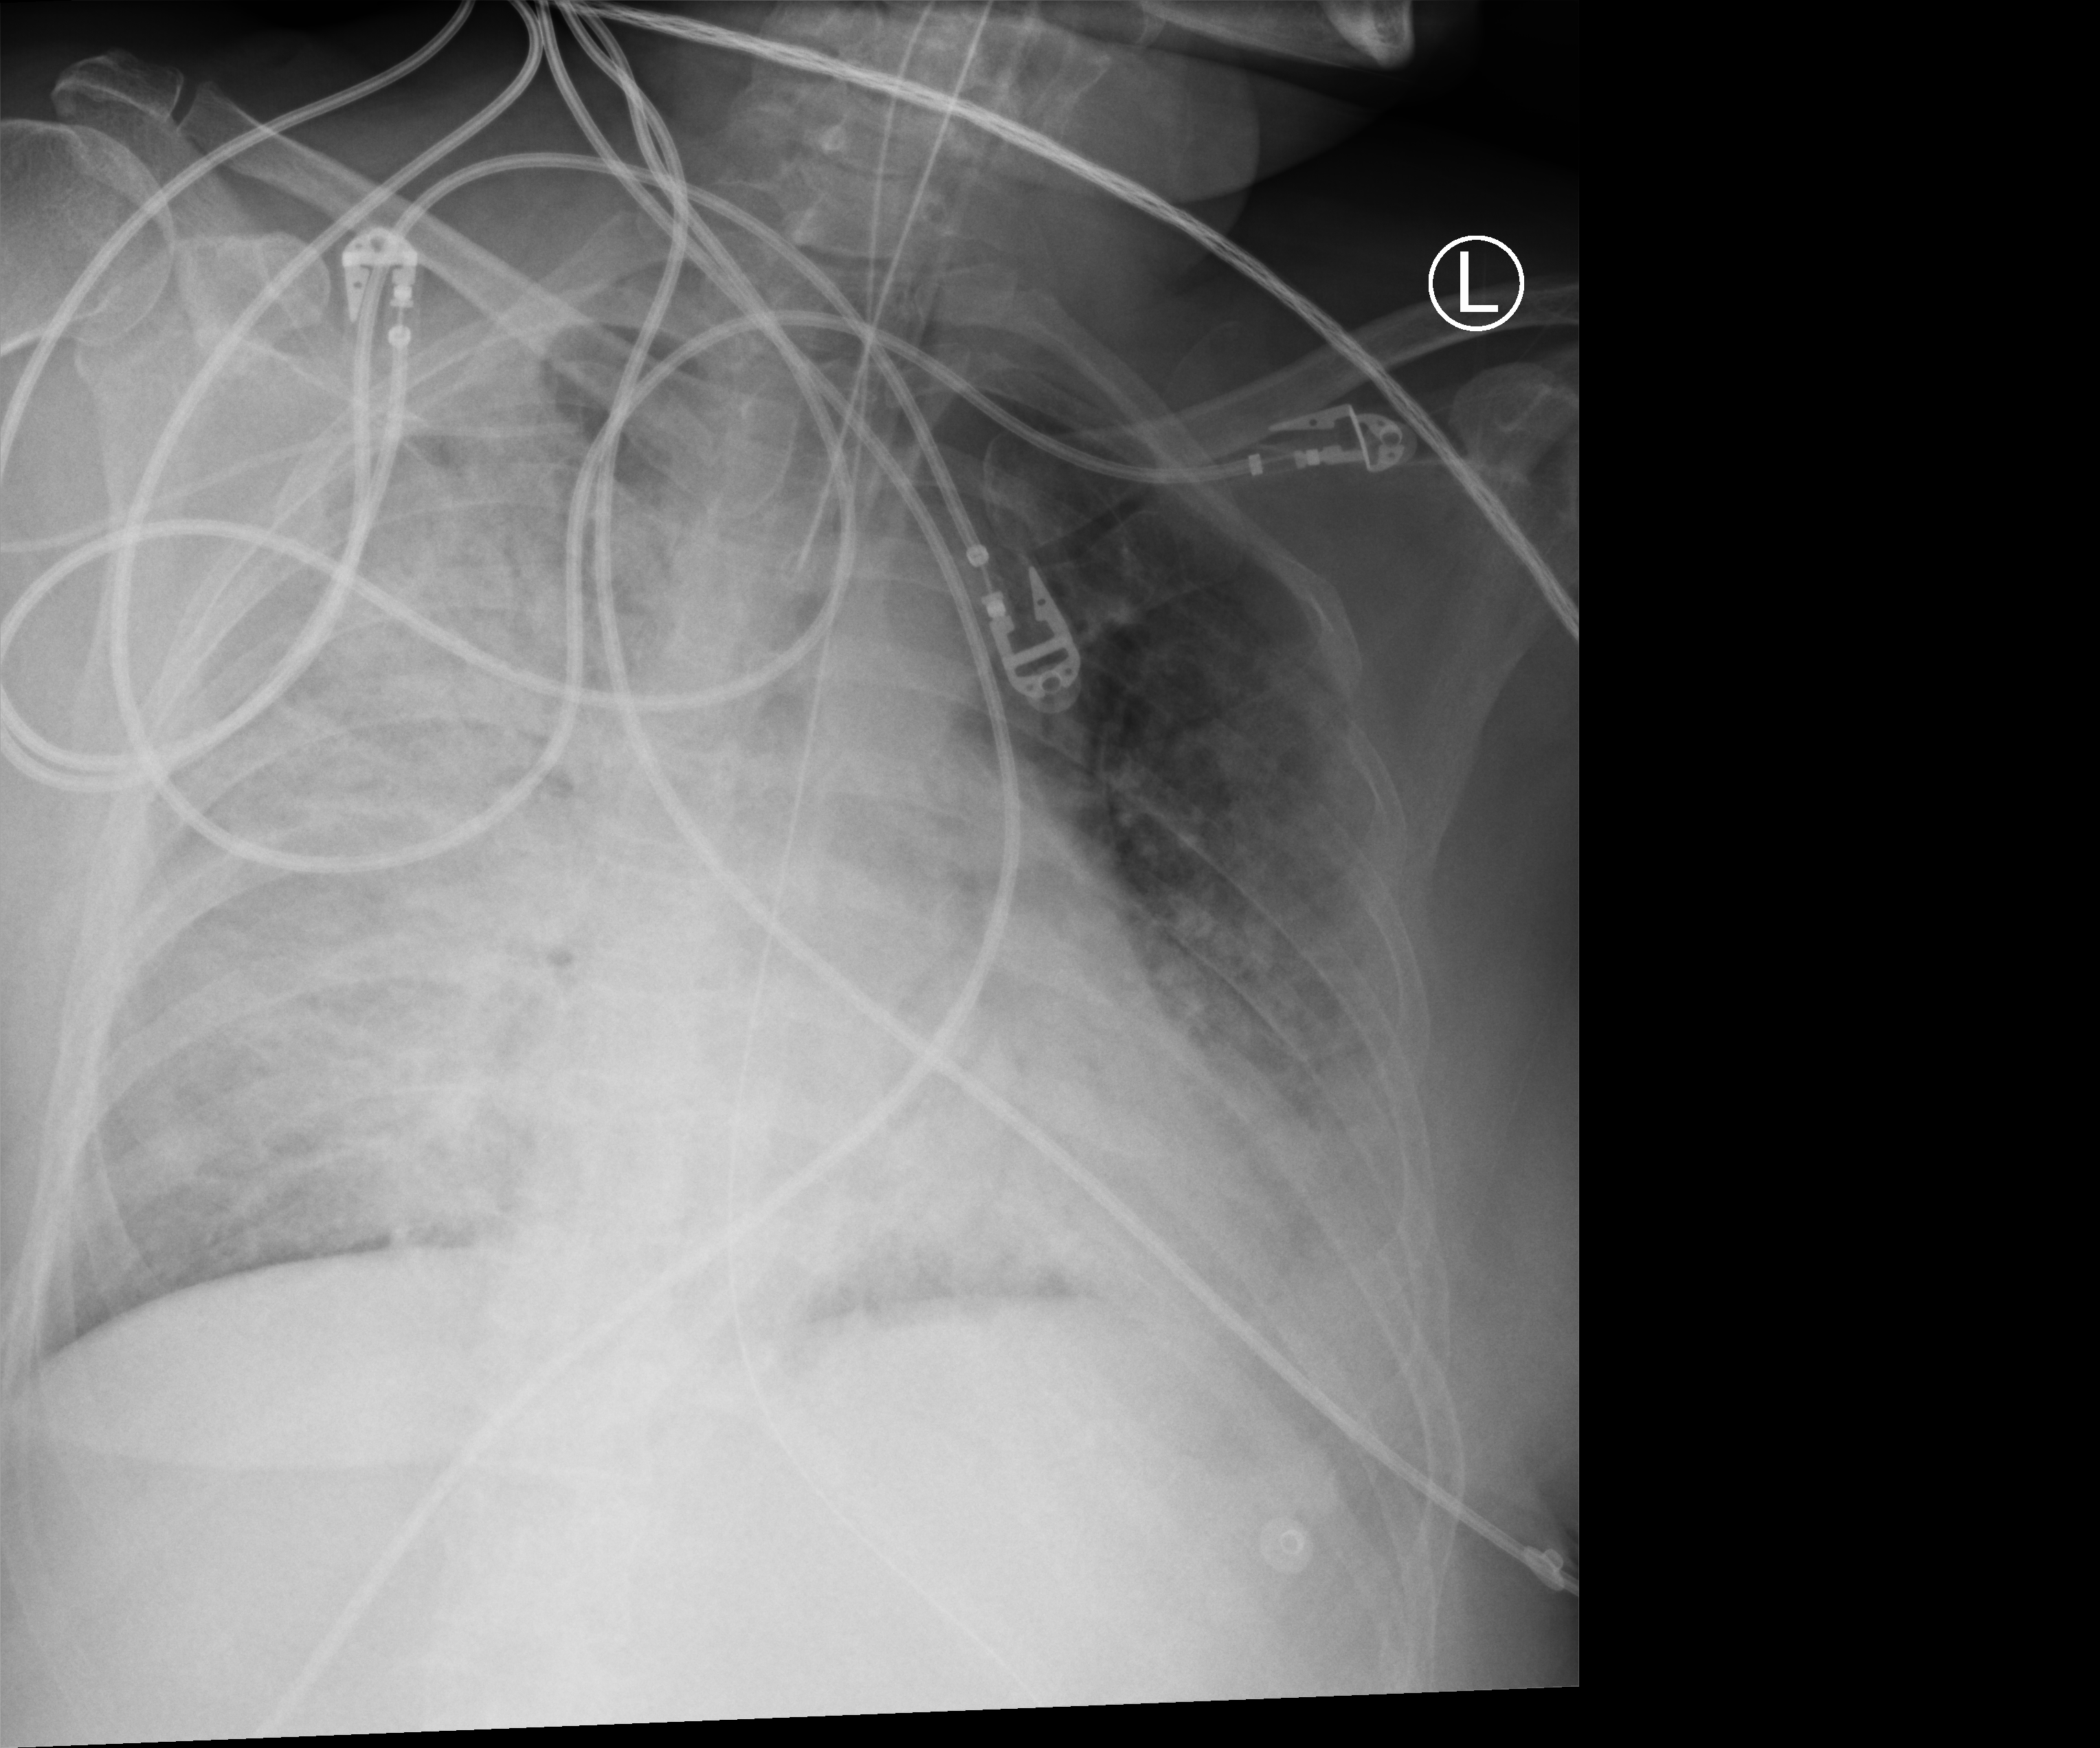
Chest X-ray (portable); anteroposterior (AP) projection. Female patient hospitalised with COVID-19, age 18–59 years.
Admission-level facts for this patient (not findings on this image; timing relative to this image not recorded): admitted to intensive care during this hospital stay: yes; mechanically ventilated during this hospital stay: yes.